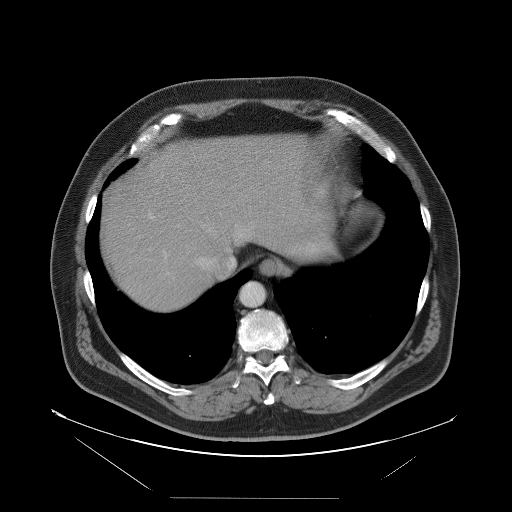
Contrast-enhanced abdominal CT, one axial slice. Position 85 of 114 along the scan axis. Intravenous contrast given. Soft-tissue window (W 400 / L 40 HU). 5 mm slice thickness. 512 × 512 image matrix, field of view 500 × 500 mm. Male patient, age 61 years. Case-level facts recorded for this patient, not image findings: diagnosis: colorectal cancer liver metastases, imaged before liver resection.
Outlined on this slice (outlined manually by an expert reader):
- hepatic veins: bounding box [x1, y1, x2, y2] px = [189, 215, 254, 270]
- liver: [101, 135, 314, 312]
- planned liver remnant (the part of the liver to remain after resection): [153, 135, 314, 261]